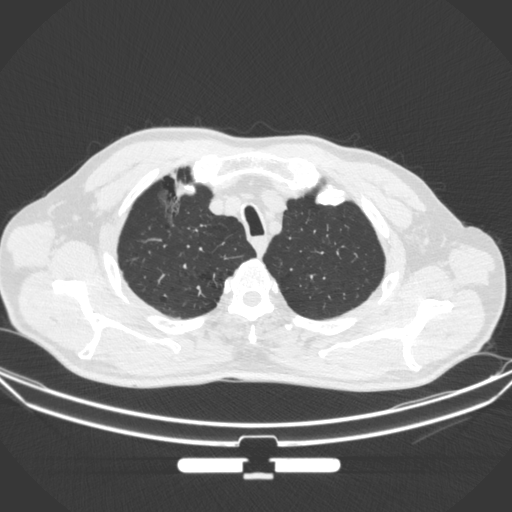
Chest CT, one axial slice; slice 295 of 355 in the series (ordered by position); 120 kVp; lung window (W 1500 / L -600 HU); 1 mm slice thickness; 512 × 512 image matrix, field of view 399 × 399 mm. Male patient, age 67 years. From the clinical record (not read from this slice): clinical TNM (as recorded): T1c N0 M0.
Outlined on this slice (bounding box drawn by a radiologist):
- lung tumour (recorded histology: adenocarcinoma): bounding box [x1, y1, x2, y2] px = [147, 185, 188, 239]